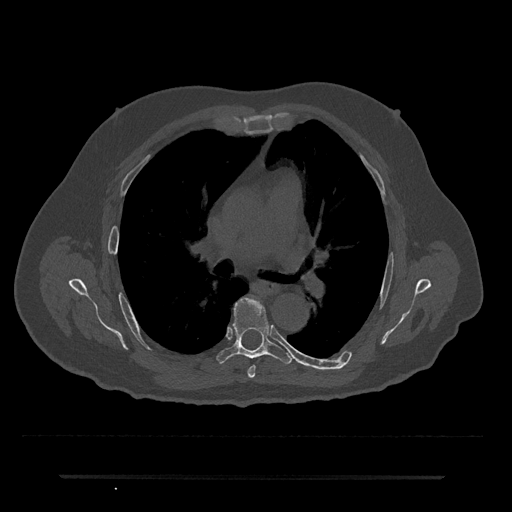
CT including the spine, one axial slice. Slice 445 of 797 in the series (ordered by position). 120 kVp. Bone window (W 1800 / L 400 HU). 512 × 512 image matrix. Male patient, age 69 years. From the clinical record (not read from this slice): primary cancer: prostate.
Annotated regions visible in this slice (semi-automatically segmented with operator editing):
- T5 vertebra: bounding box [x1, y1, x2, y2] px = [248, 365, 255, 378]
- T6 vertebra: [216, 297, 293, 364]